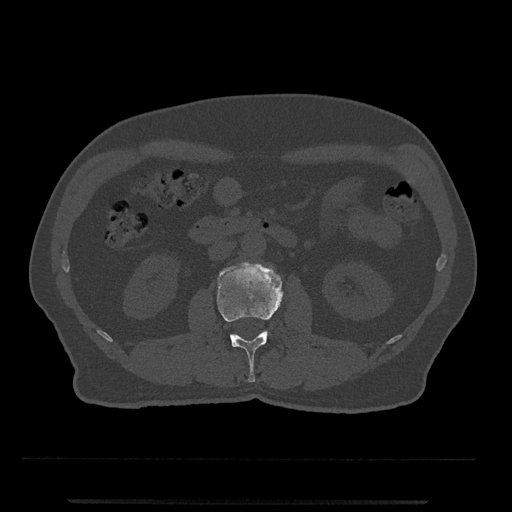
CT including the spine, one axial slice. Slice 256 of 797 in the series (ordered by position). Reconstruction kernel Br40s/3. Bone window (W 1800 / L 400 HU). 0.5 mm slice thickness. 512 × 512 image matrix, field of view 419 × 419 mm. Patient: male, 63 years. From the clinical record (not read from this slice): primary cancer: prostate.
Annotated regions visible in this slice (semi-automatic segmentation, software-assisted and operator-edited):
- L2 vertebra: bounding box (x1, y1, x2, y2) in pixels: (217, 262, 283, 382)